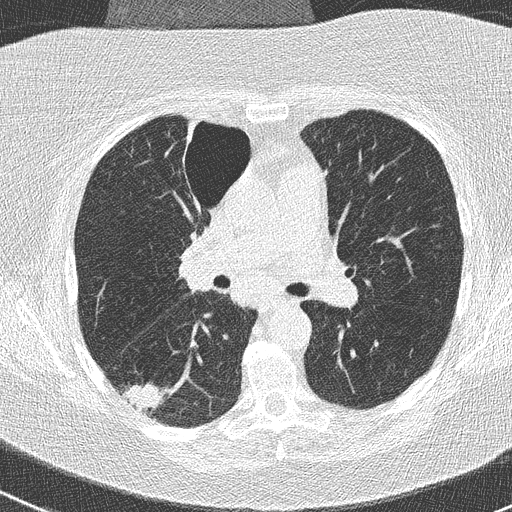
Low-dose screening chest CT, axial slice. Baseline screening round. Lung window (W 1500 / L -600 HU). 2 mm slice thickness. Lung (sharp) reconstruction kernel (B50f). 120 kVp. Slice 107 of 261 in the series. Female participant, aged 74 years at enrolment.
Expert reader's lesion annotation, bounding box (x1, y1, x2, y2) in pixels: (116, 378, 173, 425). The screening reader recorded 3 non-calcified nodules or masses ≥4 mm on this exam (right lower lobe, right upper lobe, left lower lobe); which of them this box marks is not recorded. Official screen result: positive, change unspecified: nodule(s) >= 4 mm or enlarging nodule(s), mass(es), or other non-specific abnormalities suspicious for lung cancer.